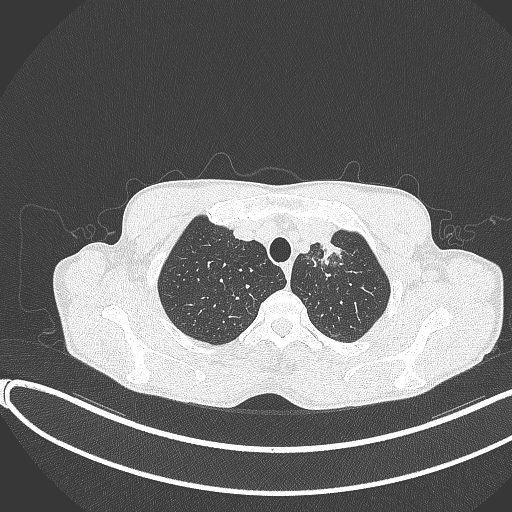
Chest CT, one axial slice. Slice 332 of 374 in the series (ordered by position). Lung window (W 1500 / L -600 HU). 1 mm slice thickness. 512 × 512 image matrix, field of view 400 × 400 mm. Patient: male, 58 years. From the clinical record (not read from this slice): clinical TNM (as recorded): T1c N1 M0.
Outlined on this slice (bounding box drawn by a radiologist):
- lung tumour (recorded histology: adenocarcinoma): bounding box (x1, y1, x2, y2) in pixels: (316, 237, 348, 274)